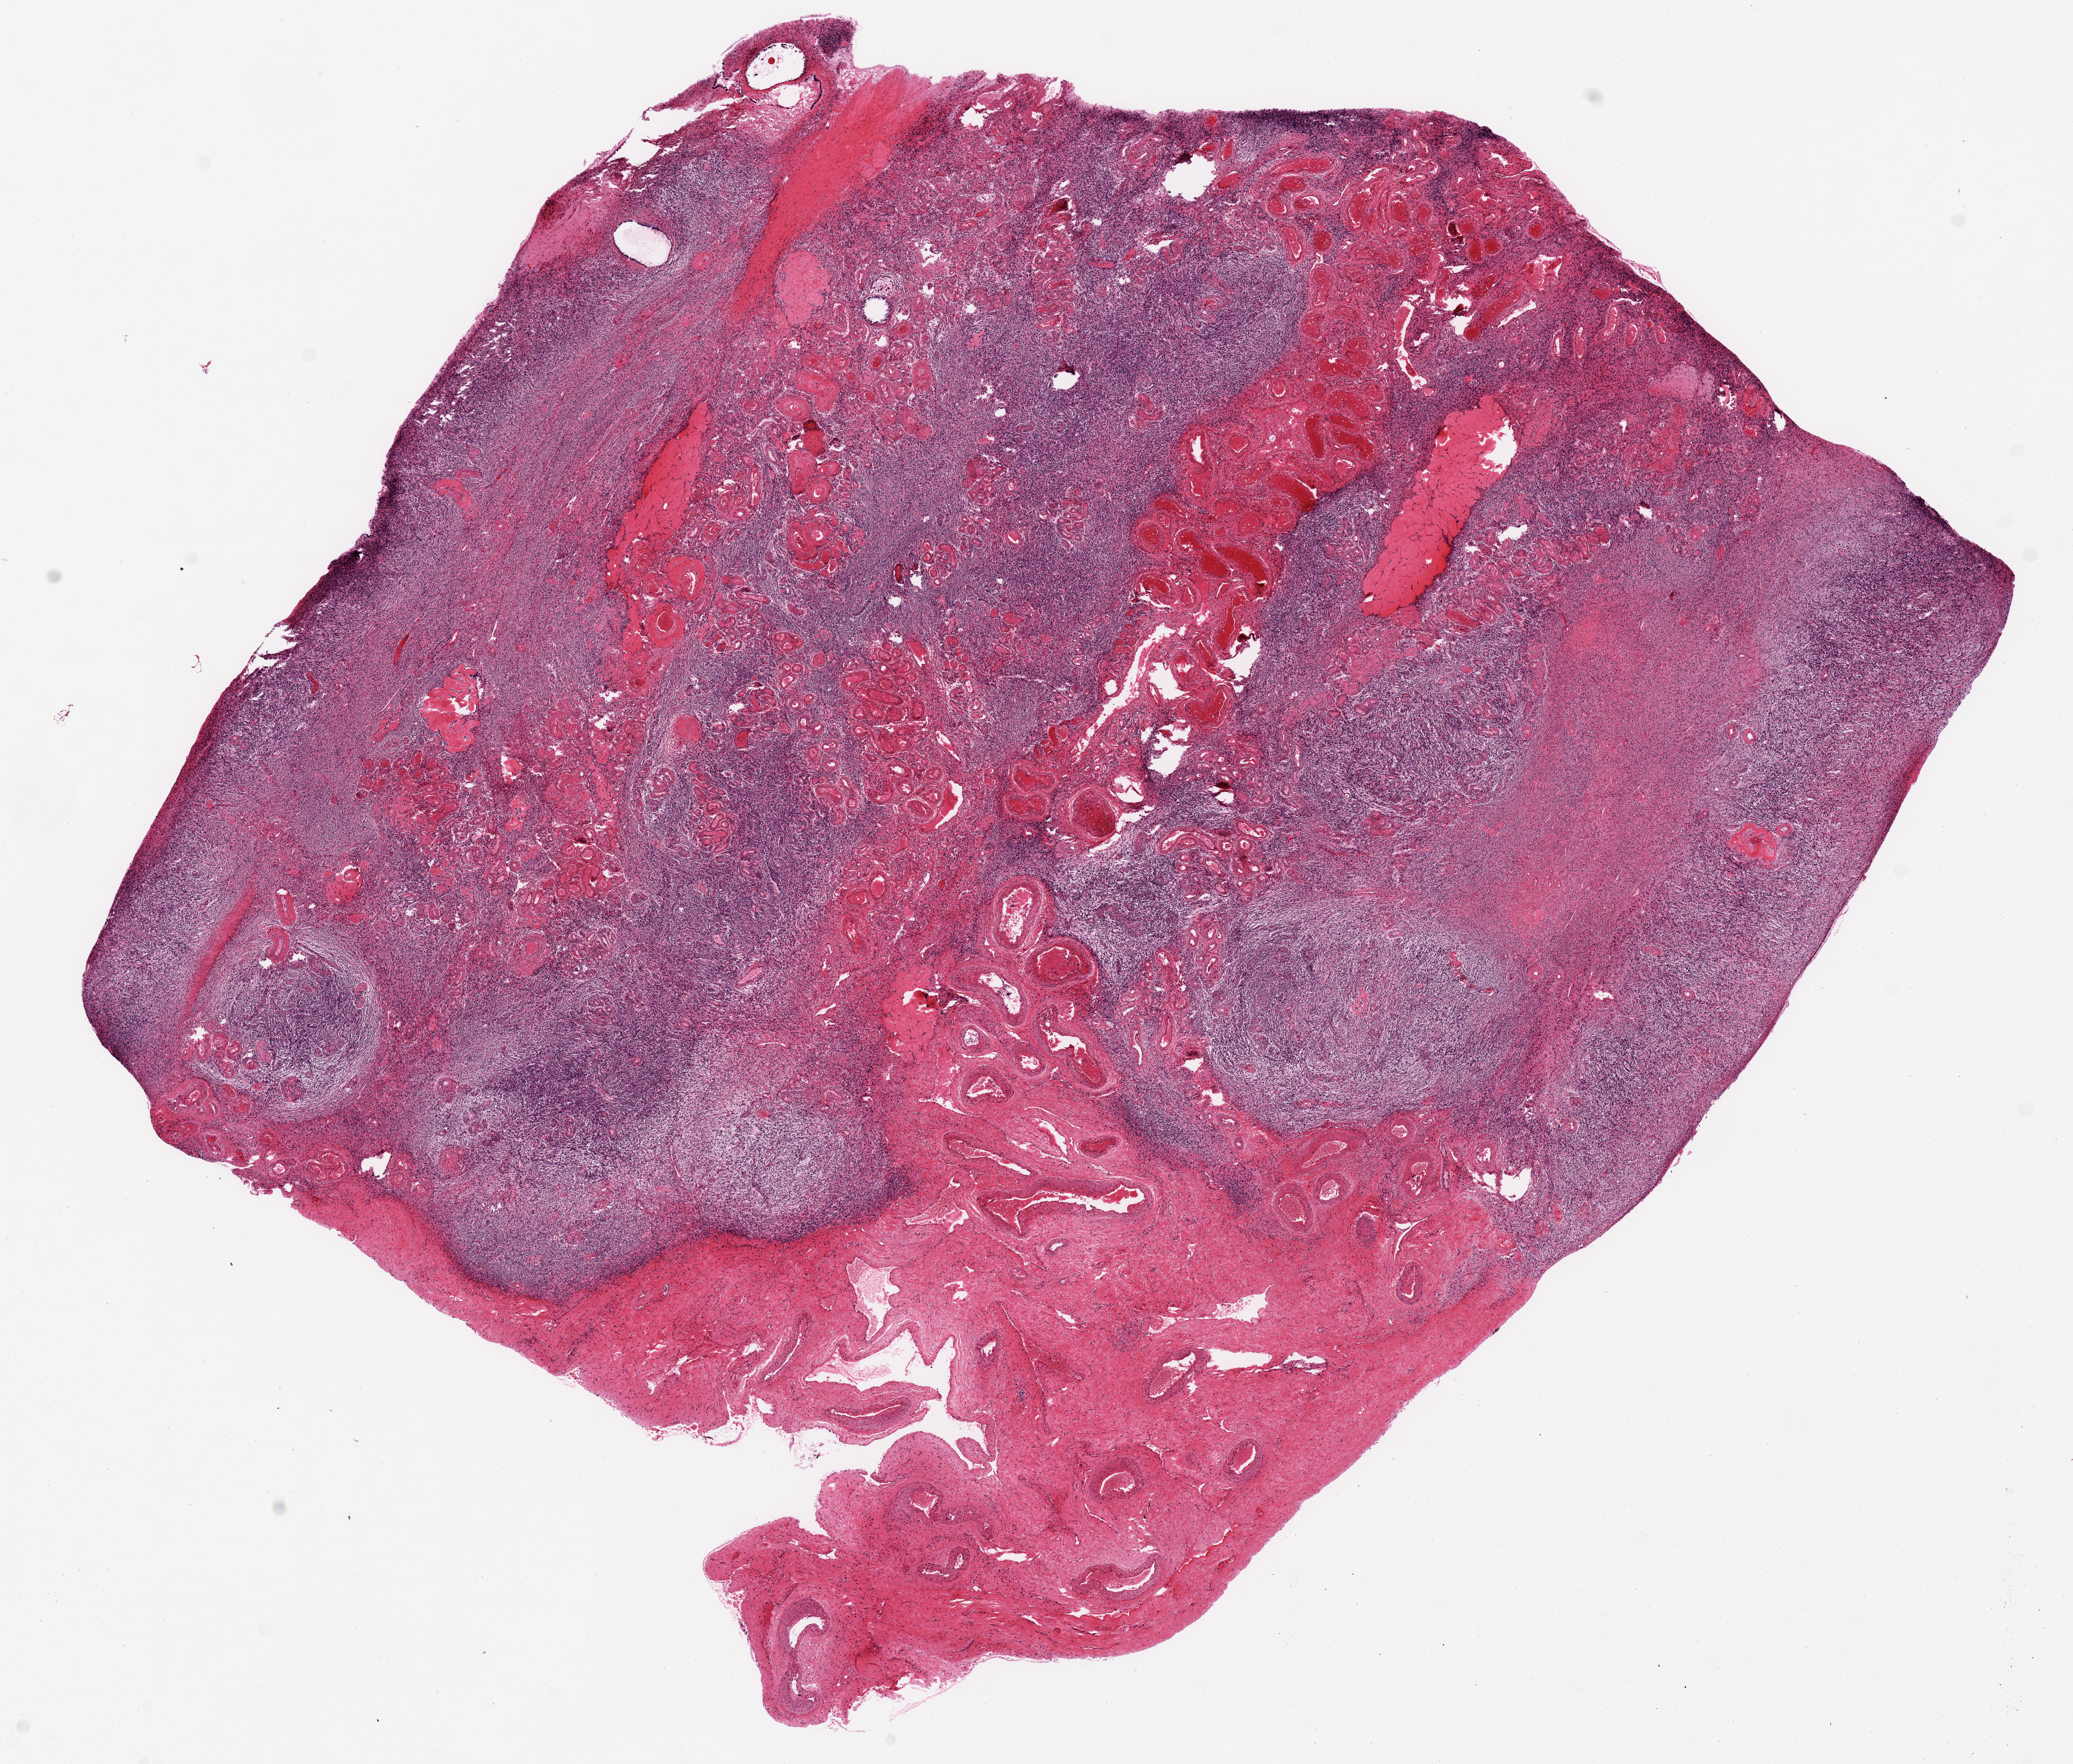
Hematoxylin and eosin (H&E) whole-slide image — whole scanned area (about 13.8 x 11.7 mm, slide scanned at 20x) shown as a low-resolution overview. PAXgene-fixed, paraffin-embedded tissue. Sampled site (target tissue): ovary. Tissue donor sample. Female donor.
Reviewer comment on this tissue sample: Atrophic. 9.5x11mm.